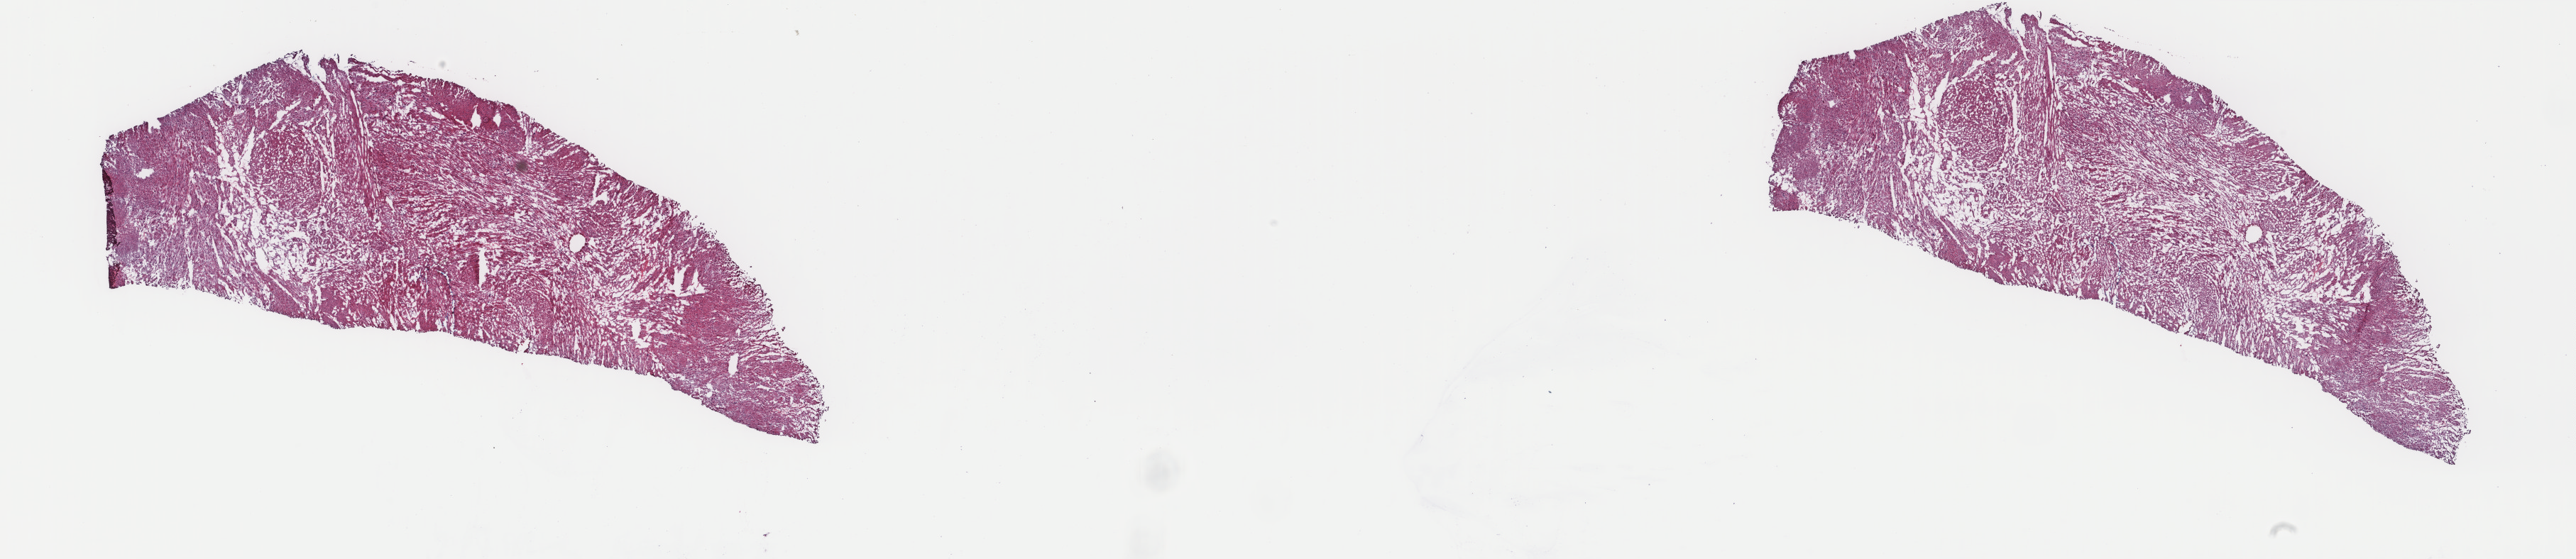
Whole-slide histology image, Hematoxylin and eosin (H&E) stained — shown as a low-resolution overview of the whole scanned area (about 28.8 x 6.3 mm), frozen section, retroperitoneum and peritoneum, primary tumour sample. Male, age 54 years at initial diagnosis. Slide review estimates, as recorded: tumour cells 100%, tumour nuclei 100%, normal cells 0%, stromal cells 0%, necrosis 0%. Inflammatory infiltration, as recorded: lymphocyte infiltration 0%, monocyte infiltration 0%, neutrophil infiltration 0%.
• pathologic diagnosis: Leiomyosarcoma, NOS (retroperitoneum)